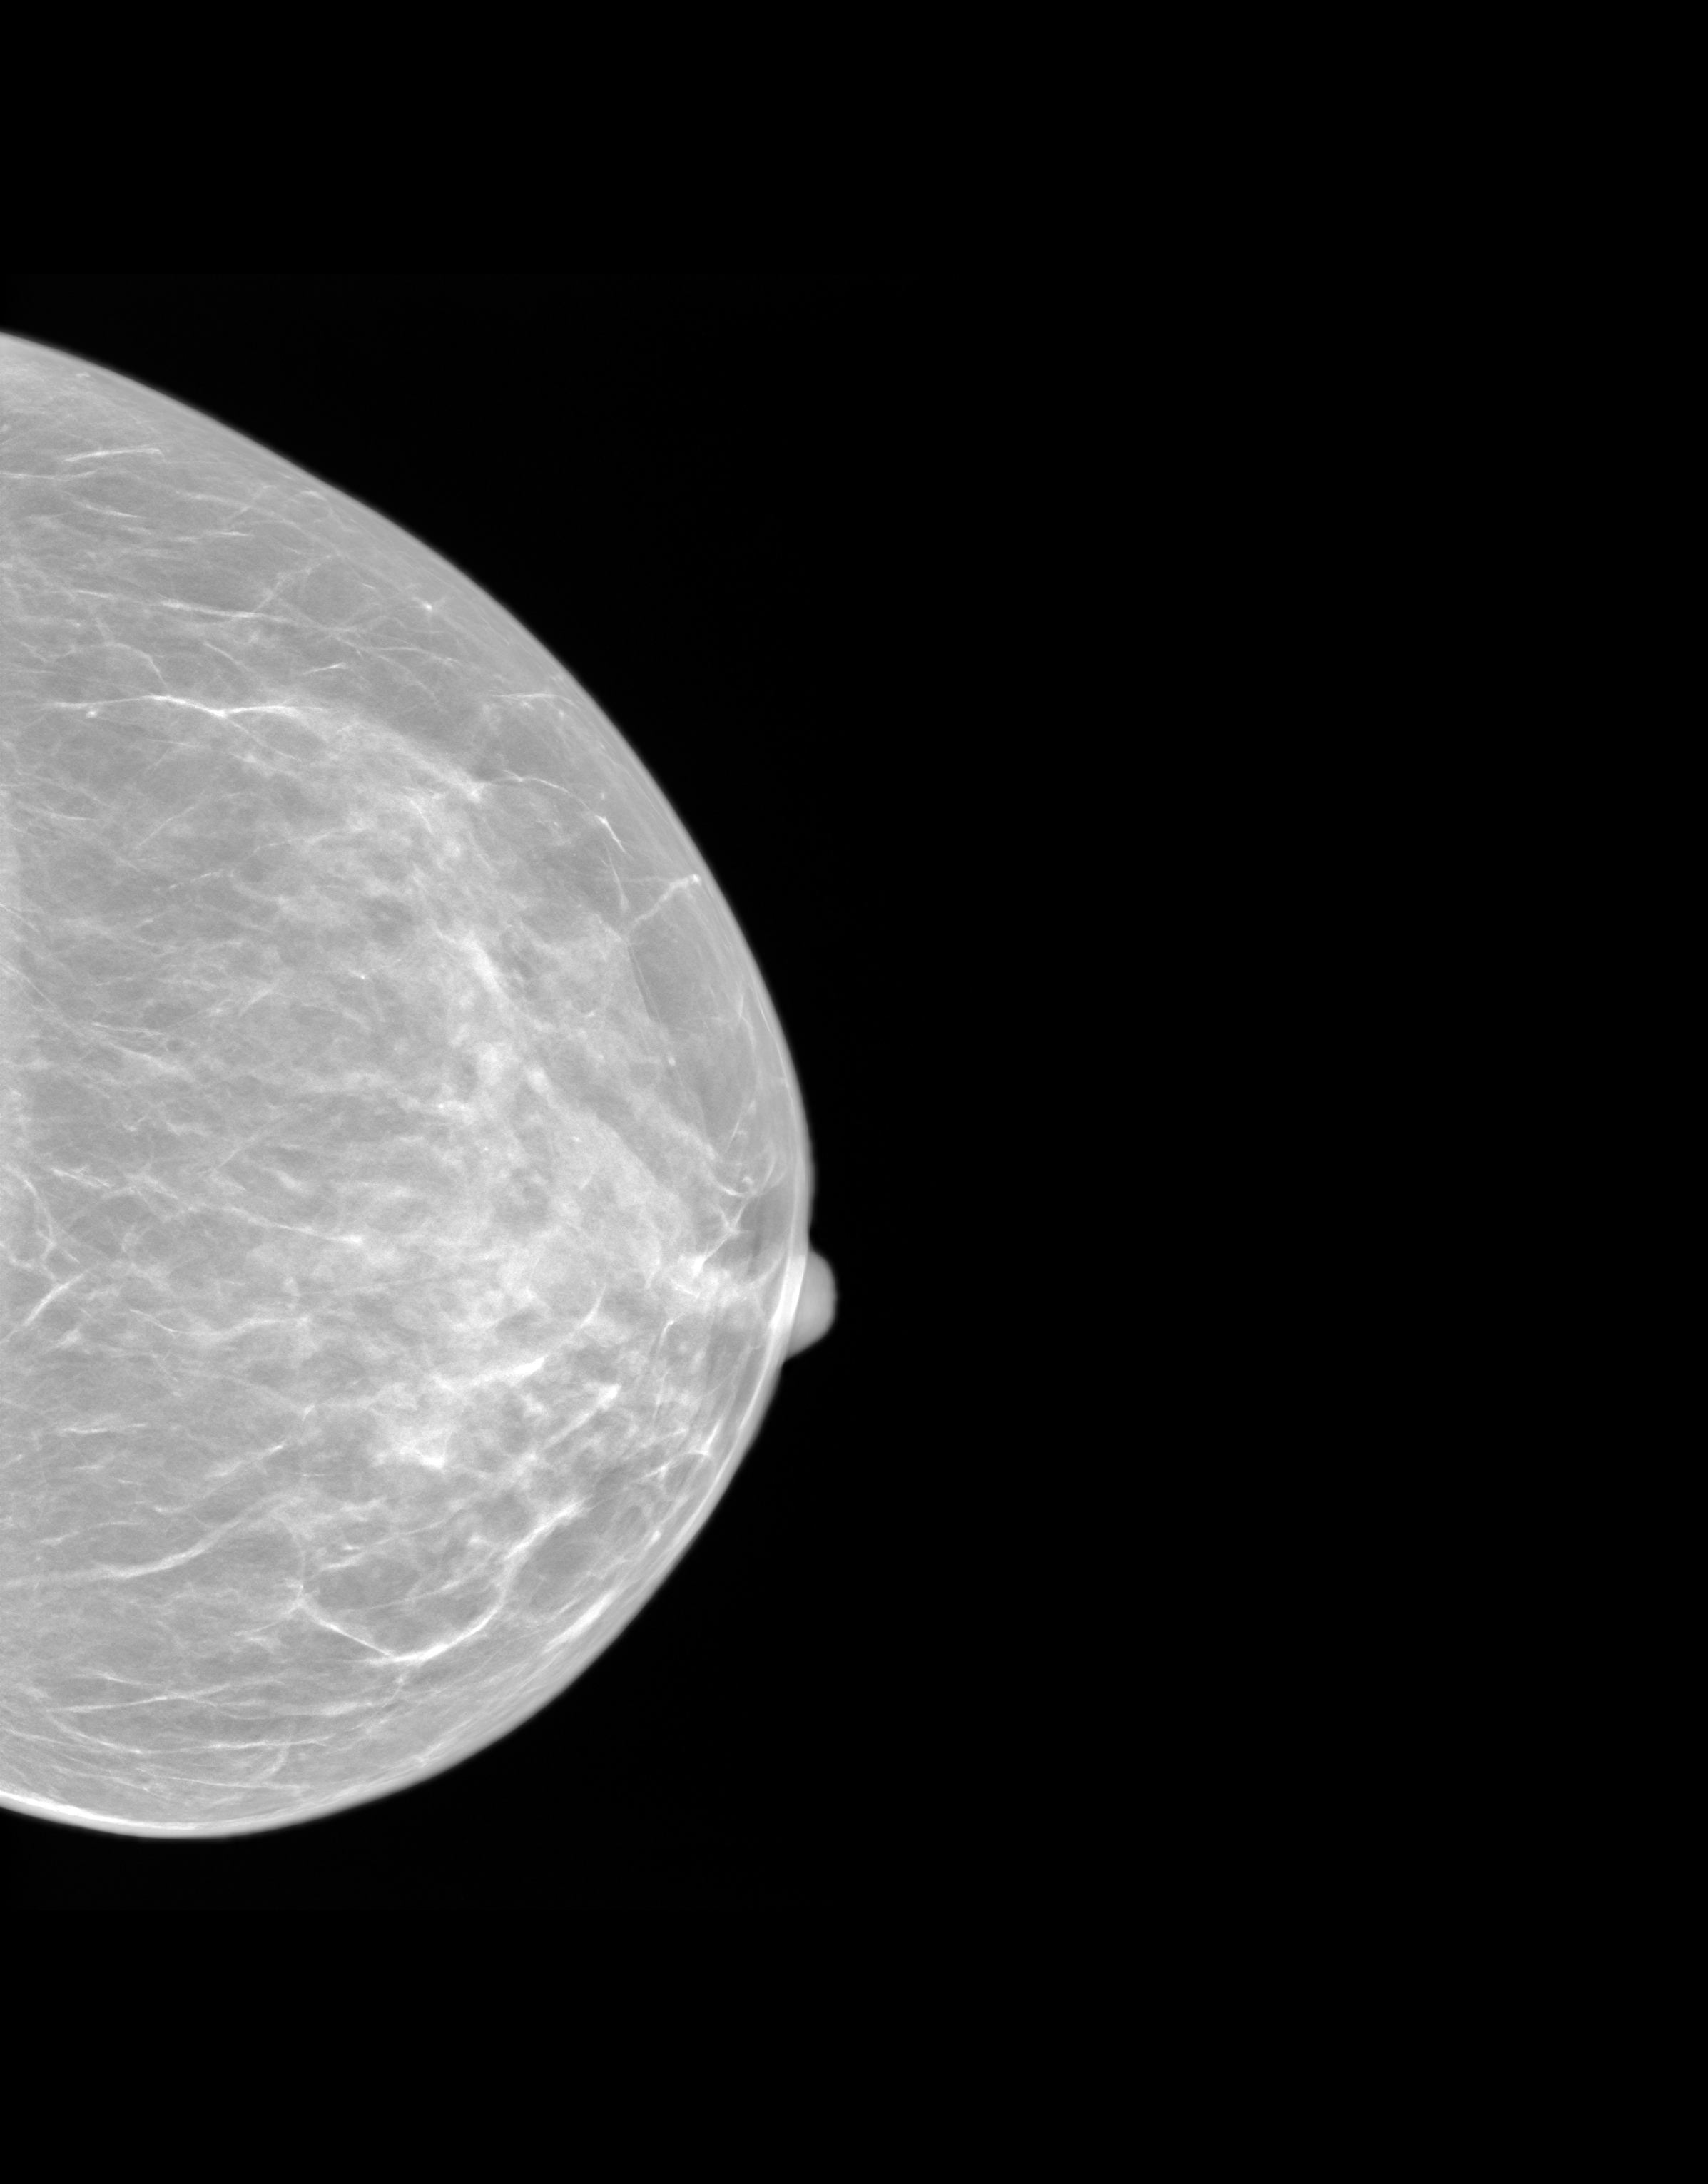
Synthetic 2-D view generated from a tomosynthesis acquisition (not an FFDM exposure), left breast, craniocaudal (CC) view, annual screening mammography examination, system: SenoIris_1SP1.1(421). Patient aged 53 years (female).
Final BI-RADS assessment for this screening round (tomosynthesis exam, both breasts): category 1.